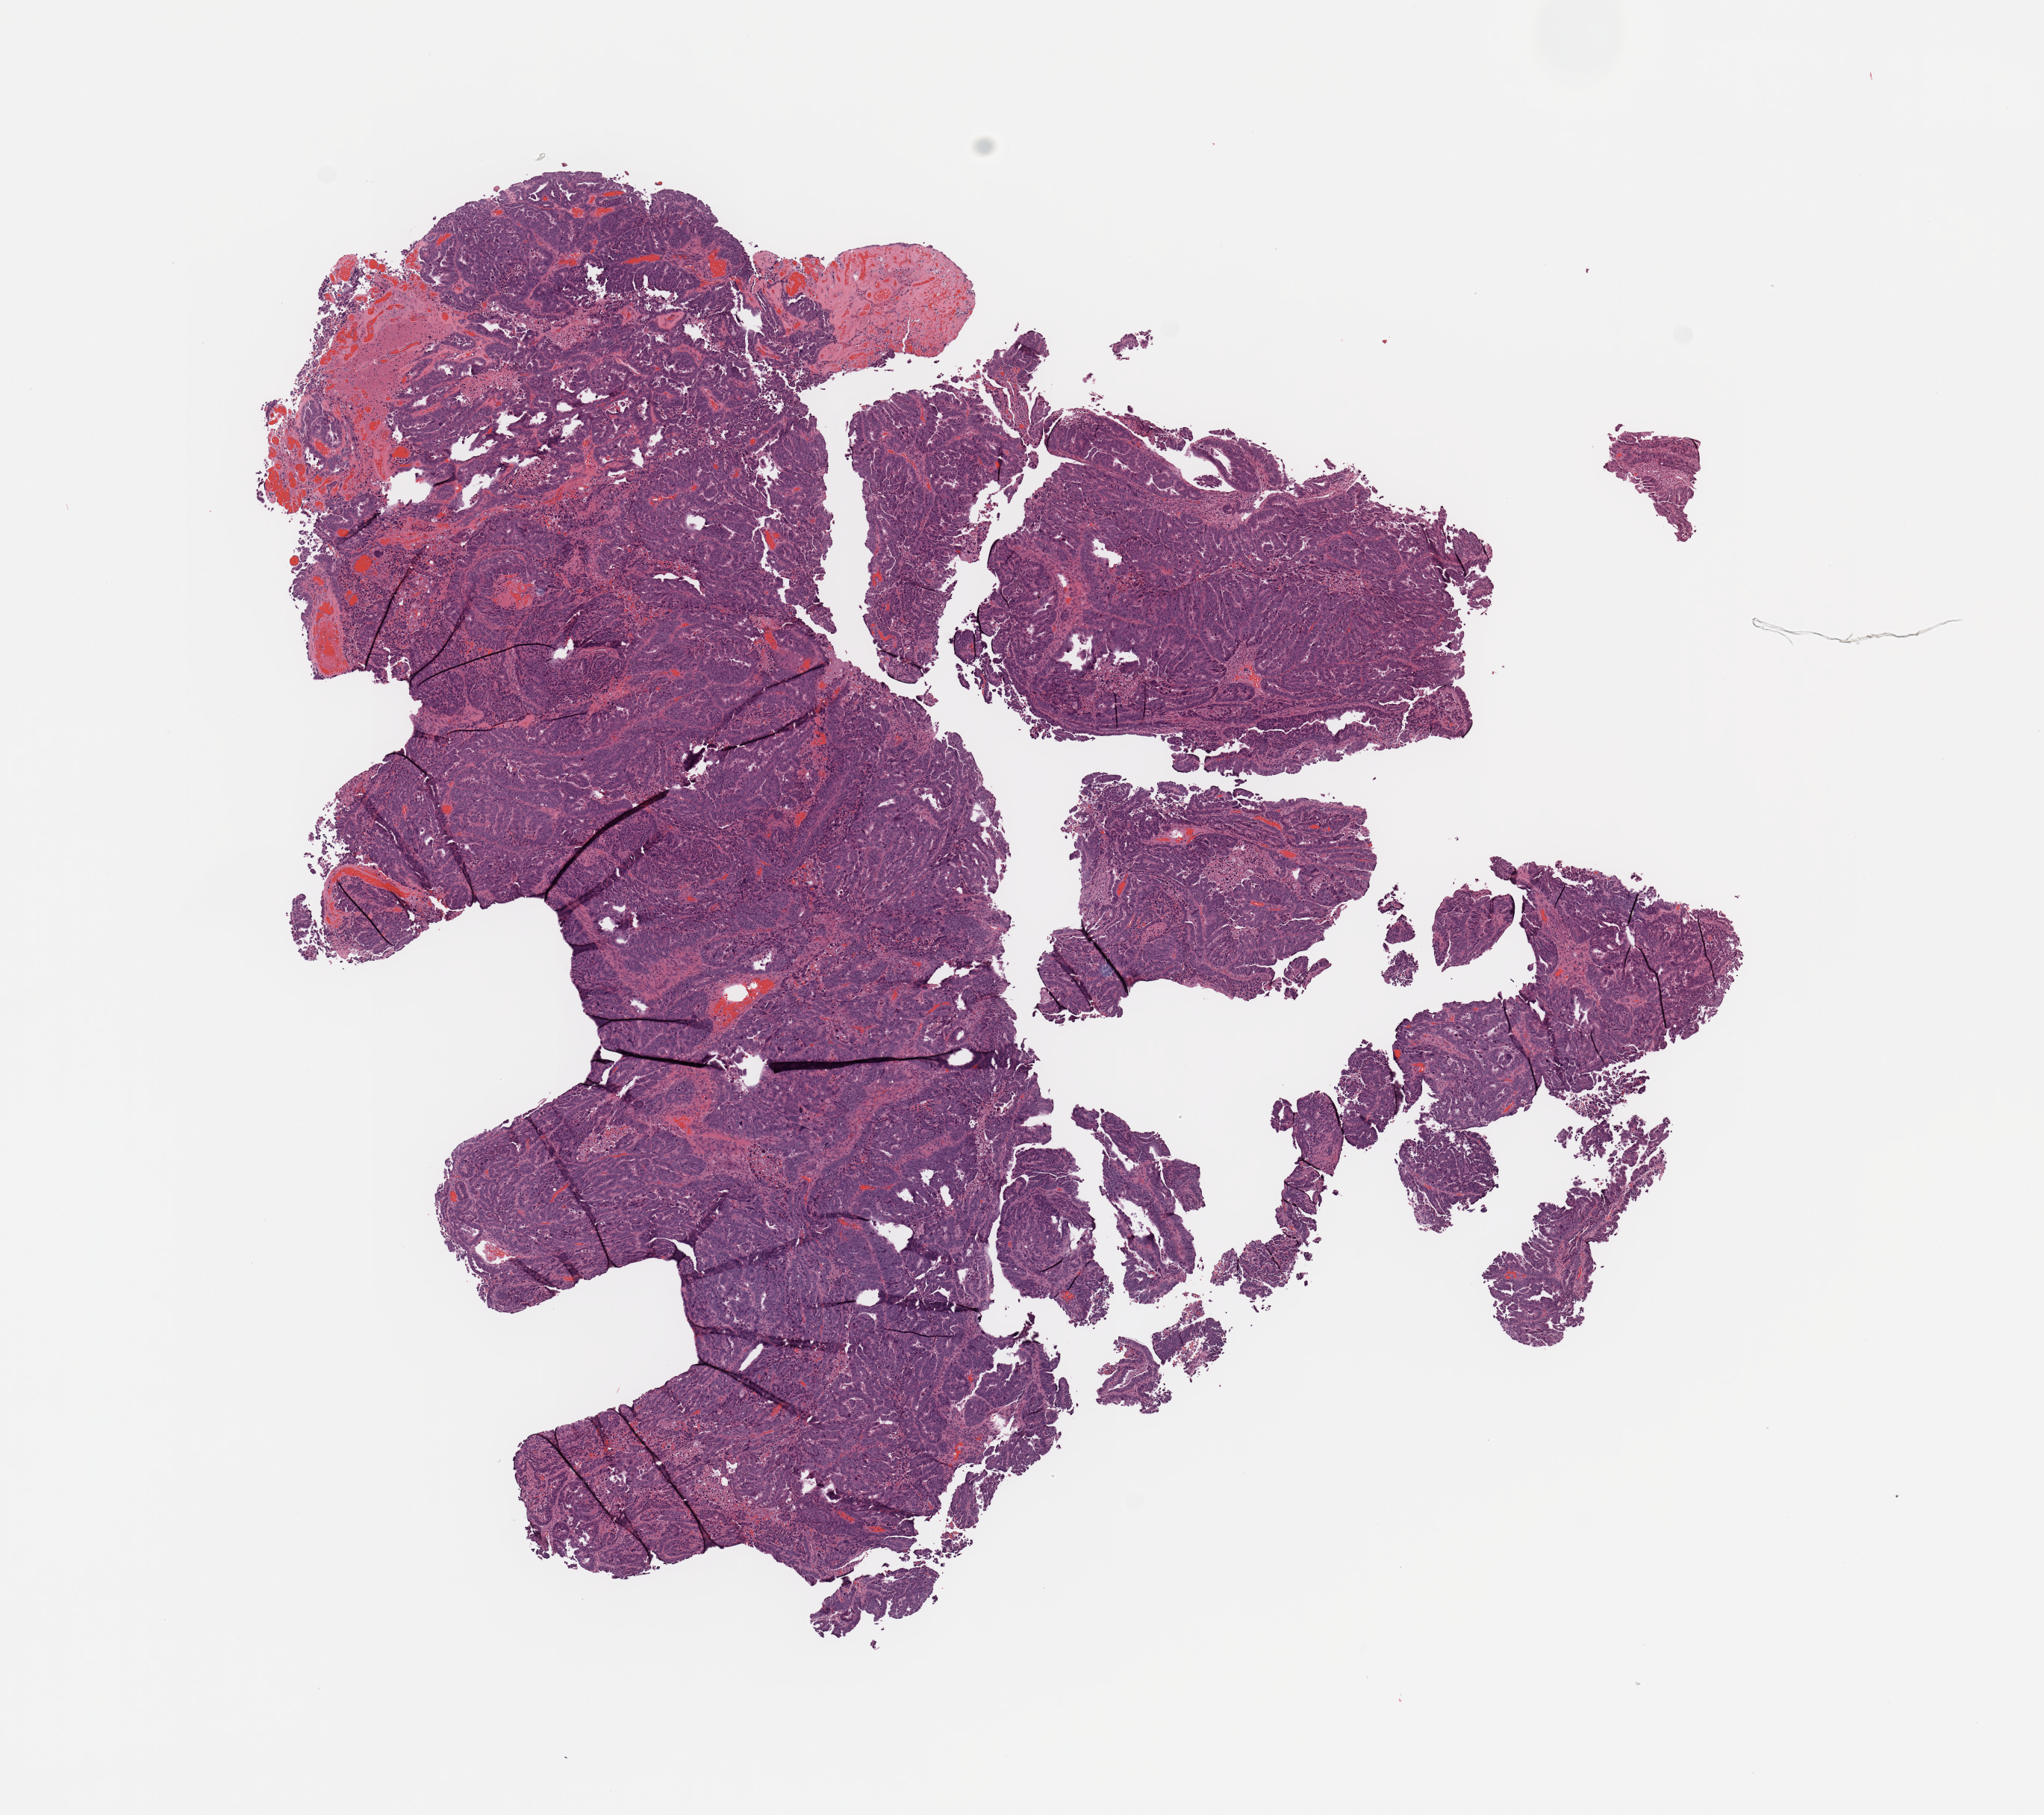
Digitized Hematoxylin and eosin (H&E) stained tissue section (whole slide) — a low-resolution overview of the entire scanned area, about 10.8 x 9.6 mm. Uterus, tumour tissue. Patient: female, age 67 years. Histologic grade: G3 (poorly differentiated).
• AJCC pathologic stage: IB
• diagnosis: Endometrioid adenocarcinoma, NOS